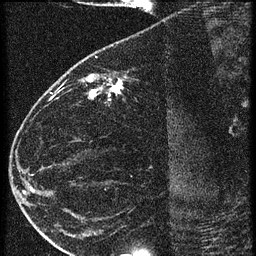
Breast MRI (dynamic contrast-enhanced), one sagittal slice; 3 images stored at this slice position (order not interpretable as contrast timing); 1.5 T; TE 4.2 ms, TR 20.4 ms; 1.5 mm slice thickness; 256 × 256 image matrix, field of view 180 × 180 mm. Female patient, age 35 years. Case-level facts recorded for this patient, not image findings: setting: breast cancer imaged before/during neoadjuvant chemotherapy; receptor status: HR-positive, HER2-negative.
Structures marked on this image (semi-automatic segmentation, software-assisted and operator-edited):
- analysis volume of interest (the breast-tissue region the enhancement analysis was run in; not a lesion): box from (x=65, y=60) to (x=169, y=119) px
- tumour enhancement mask (voxels above the 90 % enhancement threshold inside the analysis volume of interest): (x=82, y=74)–(x=126, y=99)